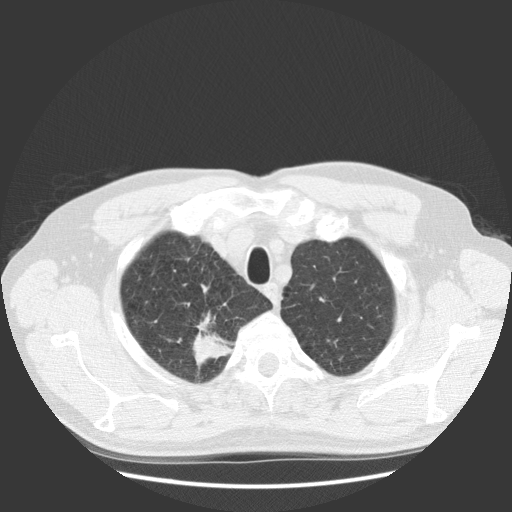
Low-dose screening chest CT, axial slice; first (baseline) screen; lung window (W 1500 / L -600 HU); 2.5 mm slice thickness. Male participant, aged 63 years at enrolment. Current smoker at enrolment.
- Expert reader's lesion annotation, bounding box <169,322,240,384> (left, top, right, bottom; pixels).
- The screening reader recorded 2 non-calcified nodules or masses ≥4 mm on this exam; which of them this box marks is not recorded.
- Lung cancer was diagnosed 30 days after this screen: squamous cell carcinoma, NOS, right upper lobe, stage IIIB (AJCC 6th edition), 35 mm at pathology.